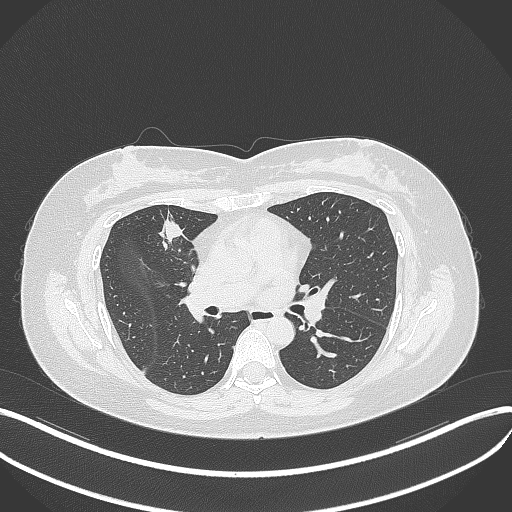
Chest CT, one axial slice. Slice 175 of 273 in the series (ordered by position). Reconstruction kernel B70f. Lung window (W 1500 / L -600 HU). 1 mm slice thickness. 512 × 512 image matrix, field of view 400 × 400 mm. Female patient, age 42 years. Case-level facts recorded for this patient, not image findings: clinical TNM (as recorded): T1b N0 M0.
Structures marked on this image (bounding box drawn by a radiologist):
- lung tumour (recorded histology: adenocarcinoma): box from (x=155, y=213) to (x=190, y=246) px